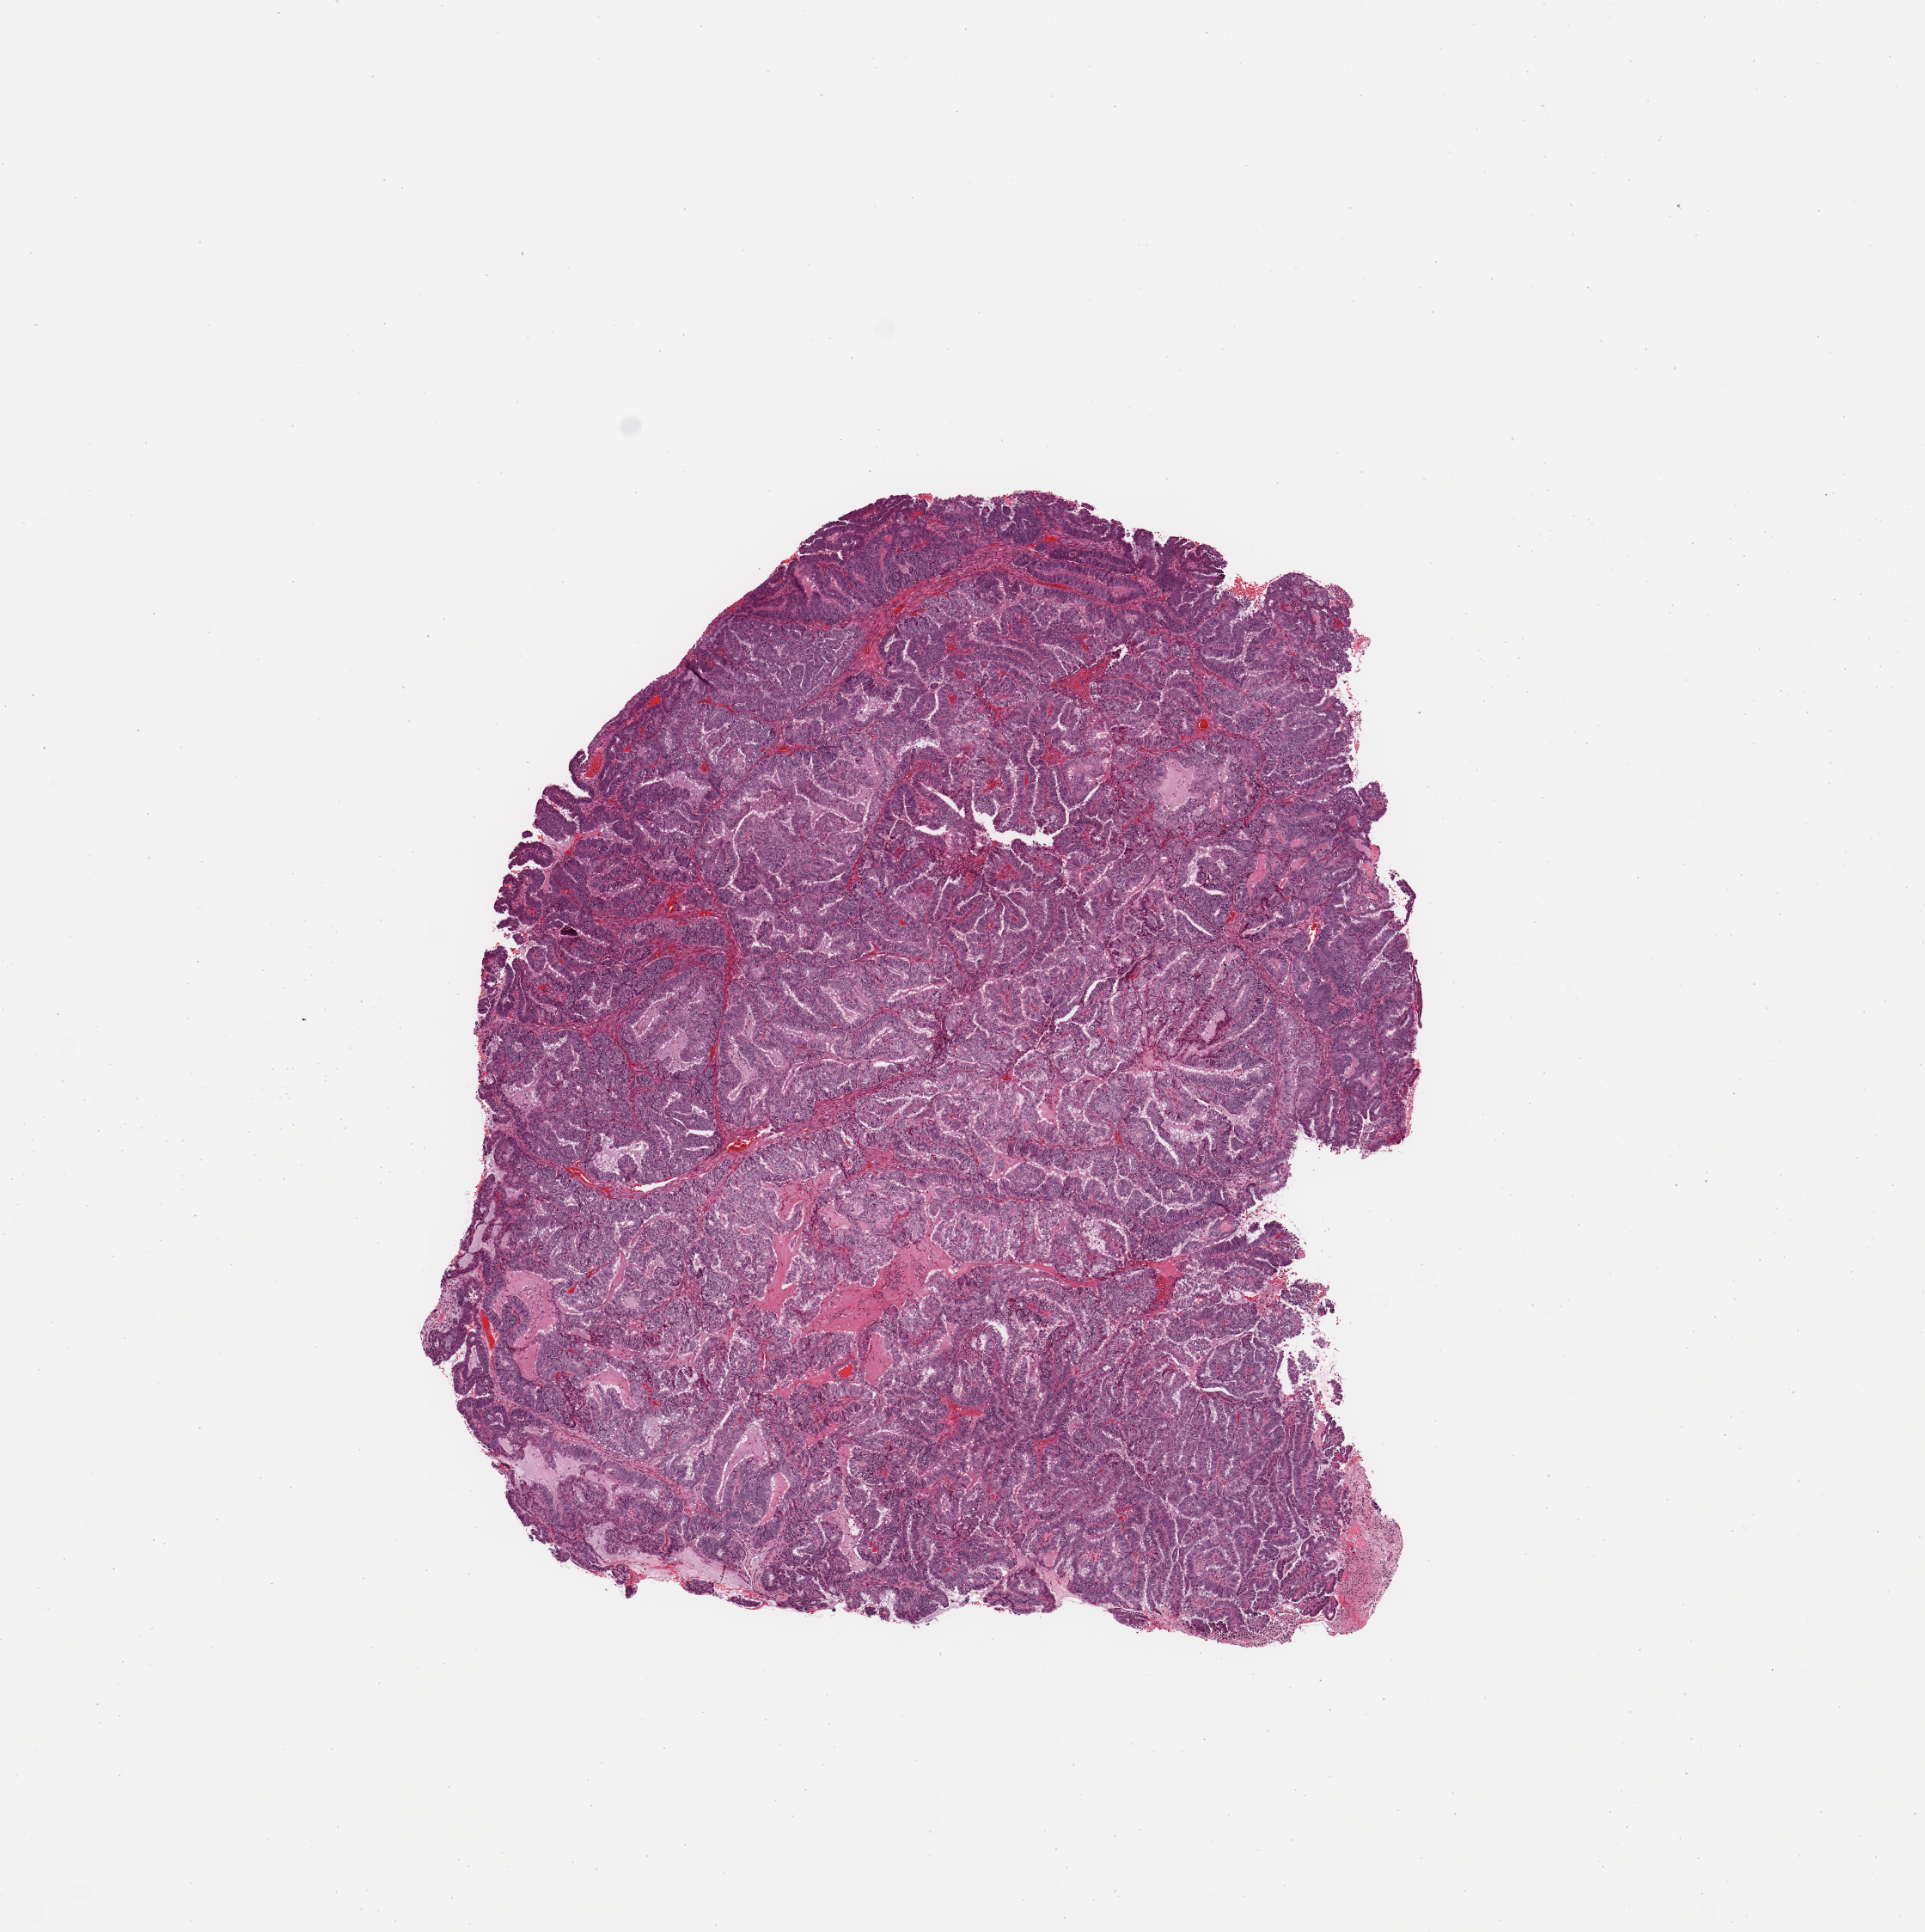
Digitized H&E tissue section (whole slide), low-resolution overview of the scanned area, about 8.9 x 8.9 mm. Uterus, tumour tissue. 80-year-old female patient. Histologic grade: G2 (moderately differentiated).
Histologic diagnosis: Endometrioid adenocarcinoma, NOS. AJCC pathologic stage: I.